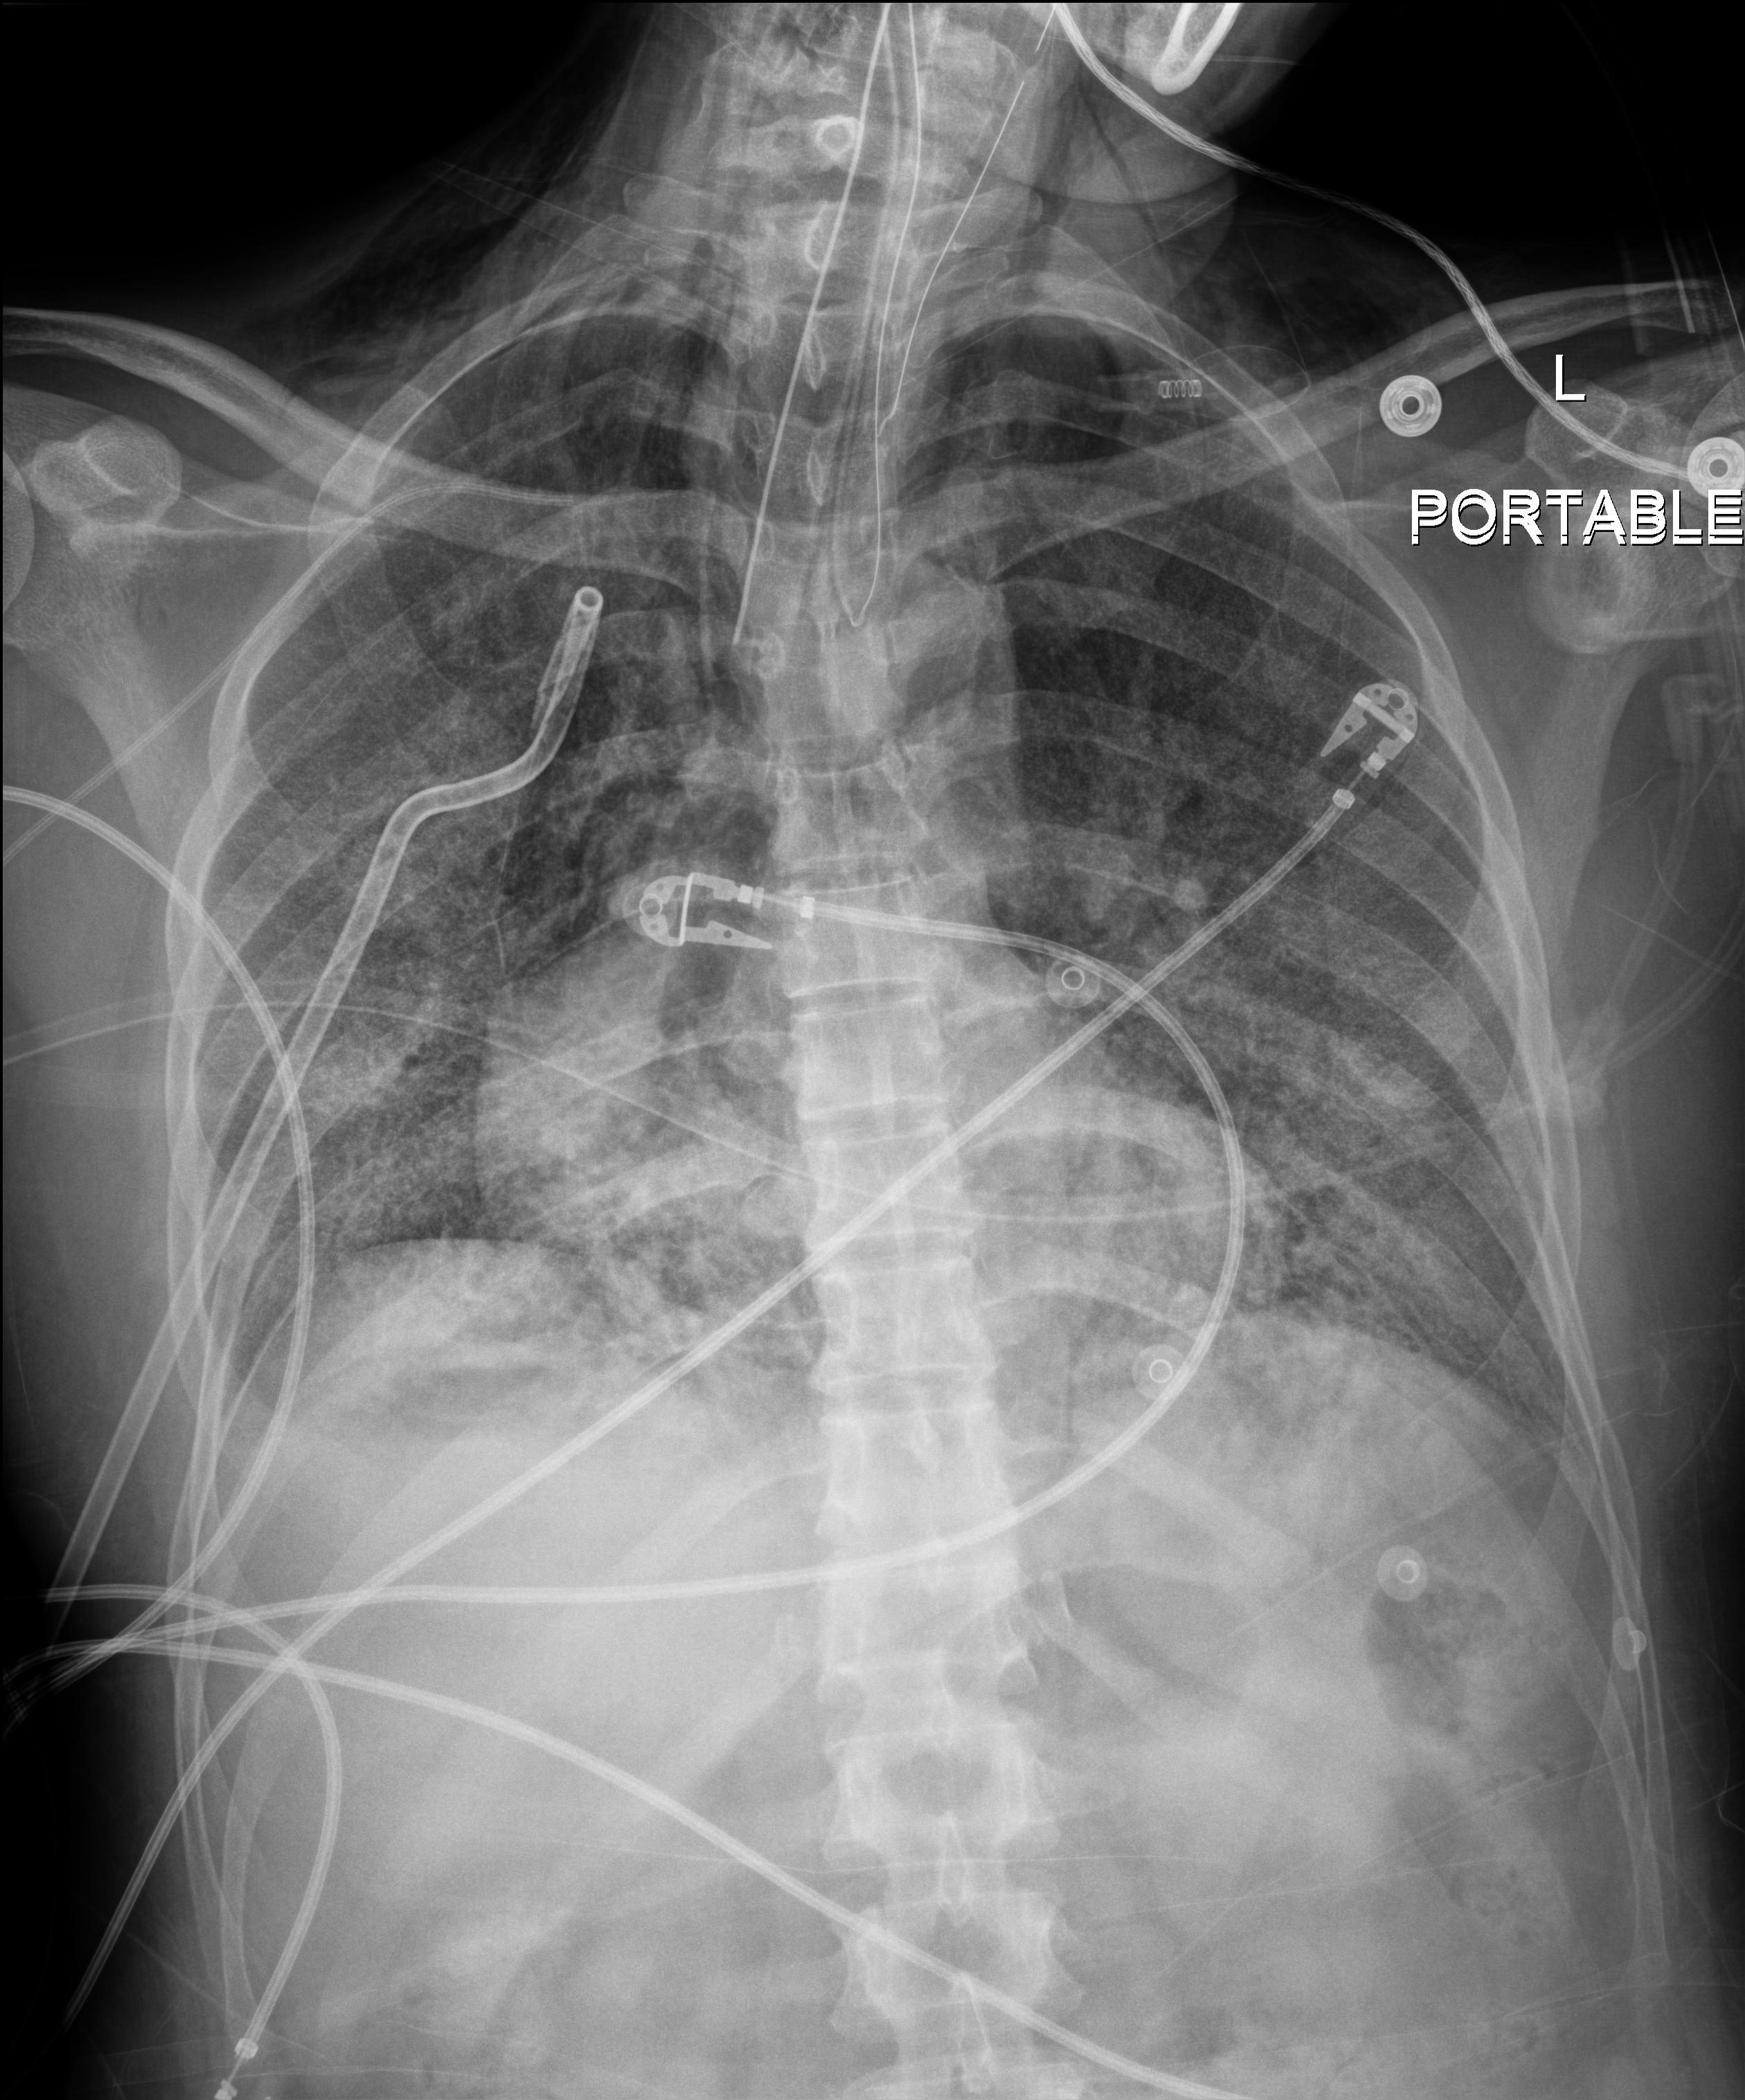
Portable chest radiograph; anteroposterior (AP) projection. Adult patient hospitalised with COVID-19, age 18–59 years.
Admission-level facts for this patient (not findings on this image; timing relative to this image not recorded): admitted to intensive care during this hospital stay: yes; diabetes (admission record): no; mechanically ventilated during this hospital stay: yes.